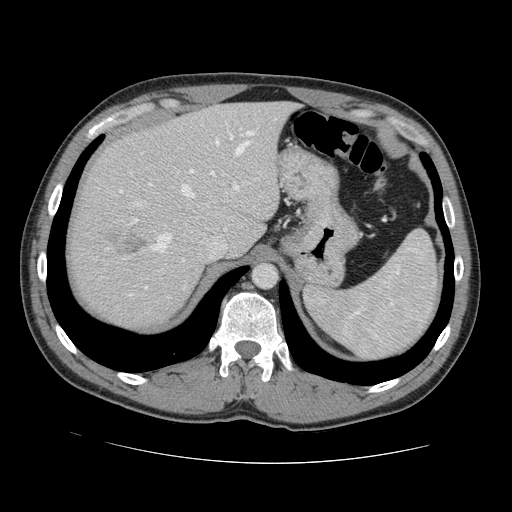
Contrast-enhanced abdominal CT, one axial slice. Intravenous contrast given. Soft-tissue window (W 400 / L 40 HU). 2.5 mm slice thickness. 512 × 512 image matrix. Male patient, age 40 years. Case-level facts recorded for this patient, not image findings: diagnosis: colorectal cancer liver metastases, imaged before liver resection; multiple liver metastases: yes; largest metastasis: 2.9 cm; chemotherapy before resection: yes.
Annotated regions visible in this slice (outlined manually by an expert reader):
- hepatic veins: box from (x=152, y=141) to (x=250, y=252) px
- liver: (x=71, y=103)–(x=291, y=326)
- planned liver remnant (the part of the liver to remain after resection): (x=98, y=102)–(x=291, y=255)
- portal vein (with intrahepatic branches): (x=189, y=132)–(x=255, y=191)
- liver metastasis: (x=120, y=235)–(x=146, y=256)